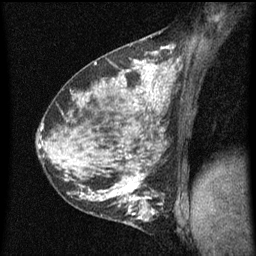
Breast MRI (dynamic contrast-enhanced), one sagittal slice. Position 33 of 60 along the scan axis. Dynamic contrast-enhanced series, image 2 of 5 at this slice position (ordered by acquisition). 1.5 T. TE 4.2 ms, TR 8 ms. 256 × 256 image matrix, field of view 180 × 180 mm. Patient: female, 35 years.
Annotated regions visible in this slice (semi-automatically segmented with operator editing):
- analysis volume of interest (the breast-tissue region the enhancement analysis was run in; not a lesion): bounding box [x1, y1, x2, y2] px = [118, 190, 165, 229]
- tumour enhancement mask (voxels above the 70 % enhancement threshold inside the analysis volume of interest): [118, 190, 156, 221]